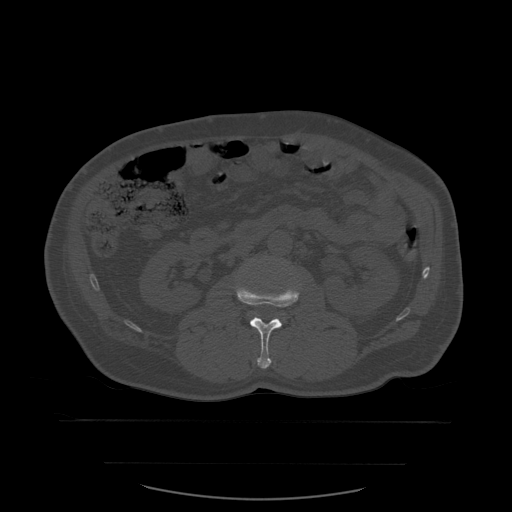
CT including the spine, one axial slice. Slice 212 of 590 in the series (ordered by position). Bone window (W 1800 / L 400 HU). 512 × 512 image matrix, field of view 479 × 479 mm. Patient age 71 years. Case-level facts recorded for this patient, not image findings: primary cancer: lung; vertebrae with lytic lesions (as recorded): T1, T2, L5, S1.
Outlined on this slice (semi-automatically segmented with operator editing):
- L2 vertebra: box from (x=236, y=274) to (x=300, y=369) px